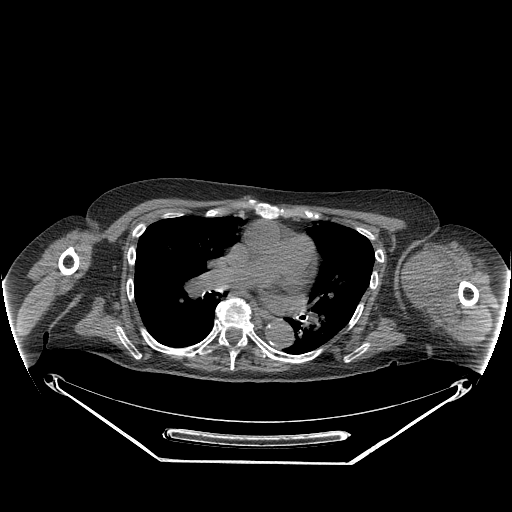
CT of an extremity soft-tissue mass (from a PET/CT study), one axial slice; reconstruction kernel STANDARD; 140 kVp; soft-tissue window (W 400 / L 40 HU); 3.75 mm slice thickness; 512 × 512 image matrix. Female patient. Case-level facts recorded for this patient, not image findings: histological type: pleiomorphic leiomyosarcoma; grade: high; site of the primary tumour: left biceps.
Annotated regions visible in this slice (expert contour drawn on MRI and transferred to this co-registered scan by the dataset authors):
- gross tumour volume including surrounding oedema: bounding box [x1, y1, x2, y2] px = [407, 246, 462, 323]
- gross tumour volume (mass): [407, 246, 460, 307]